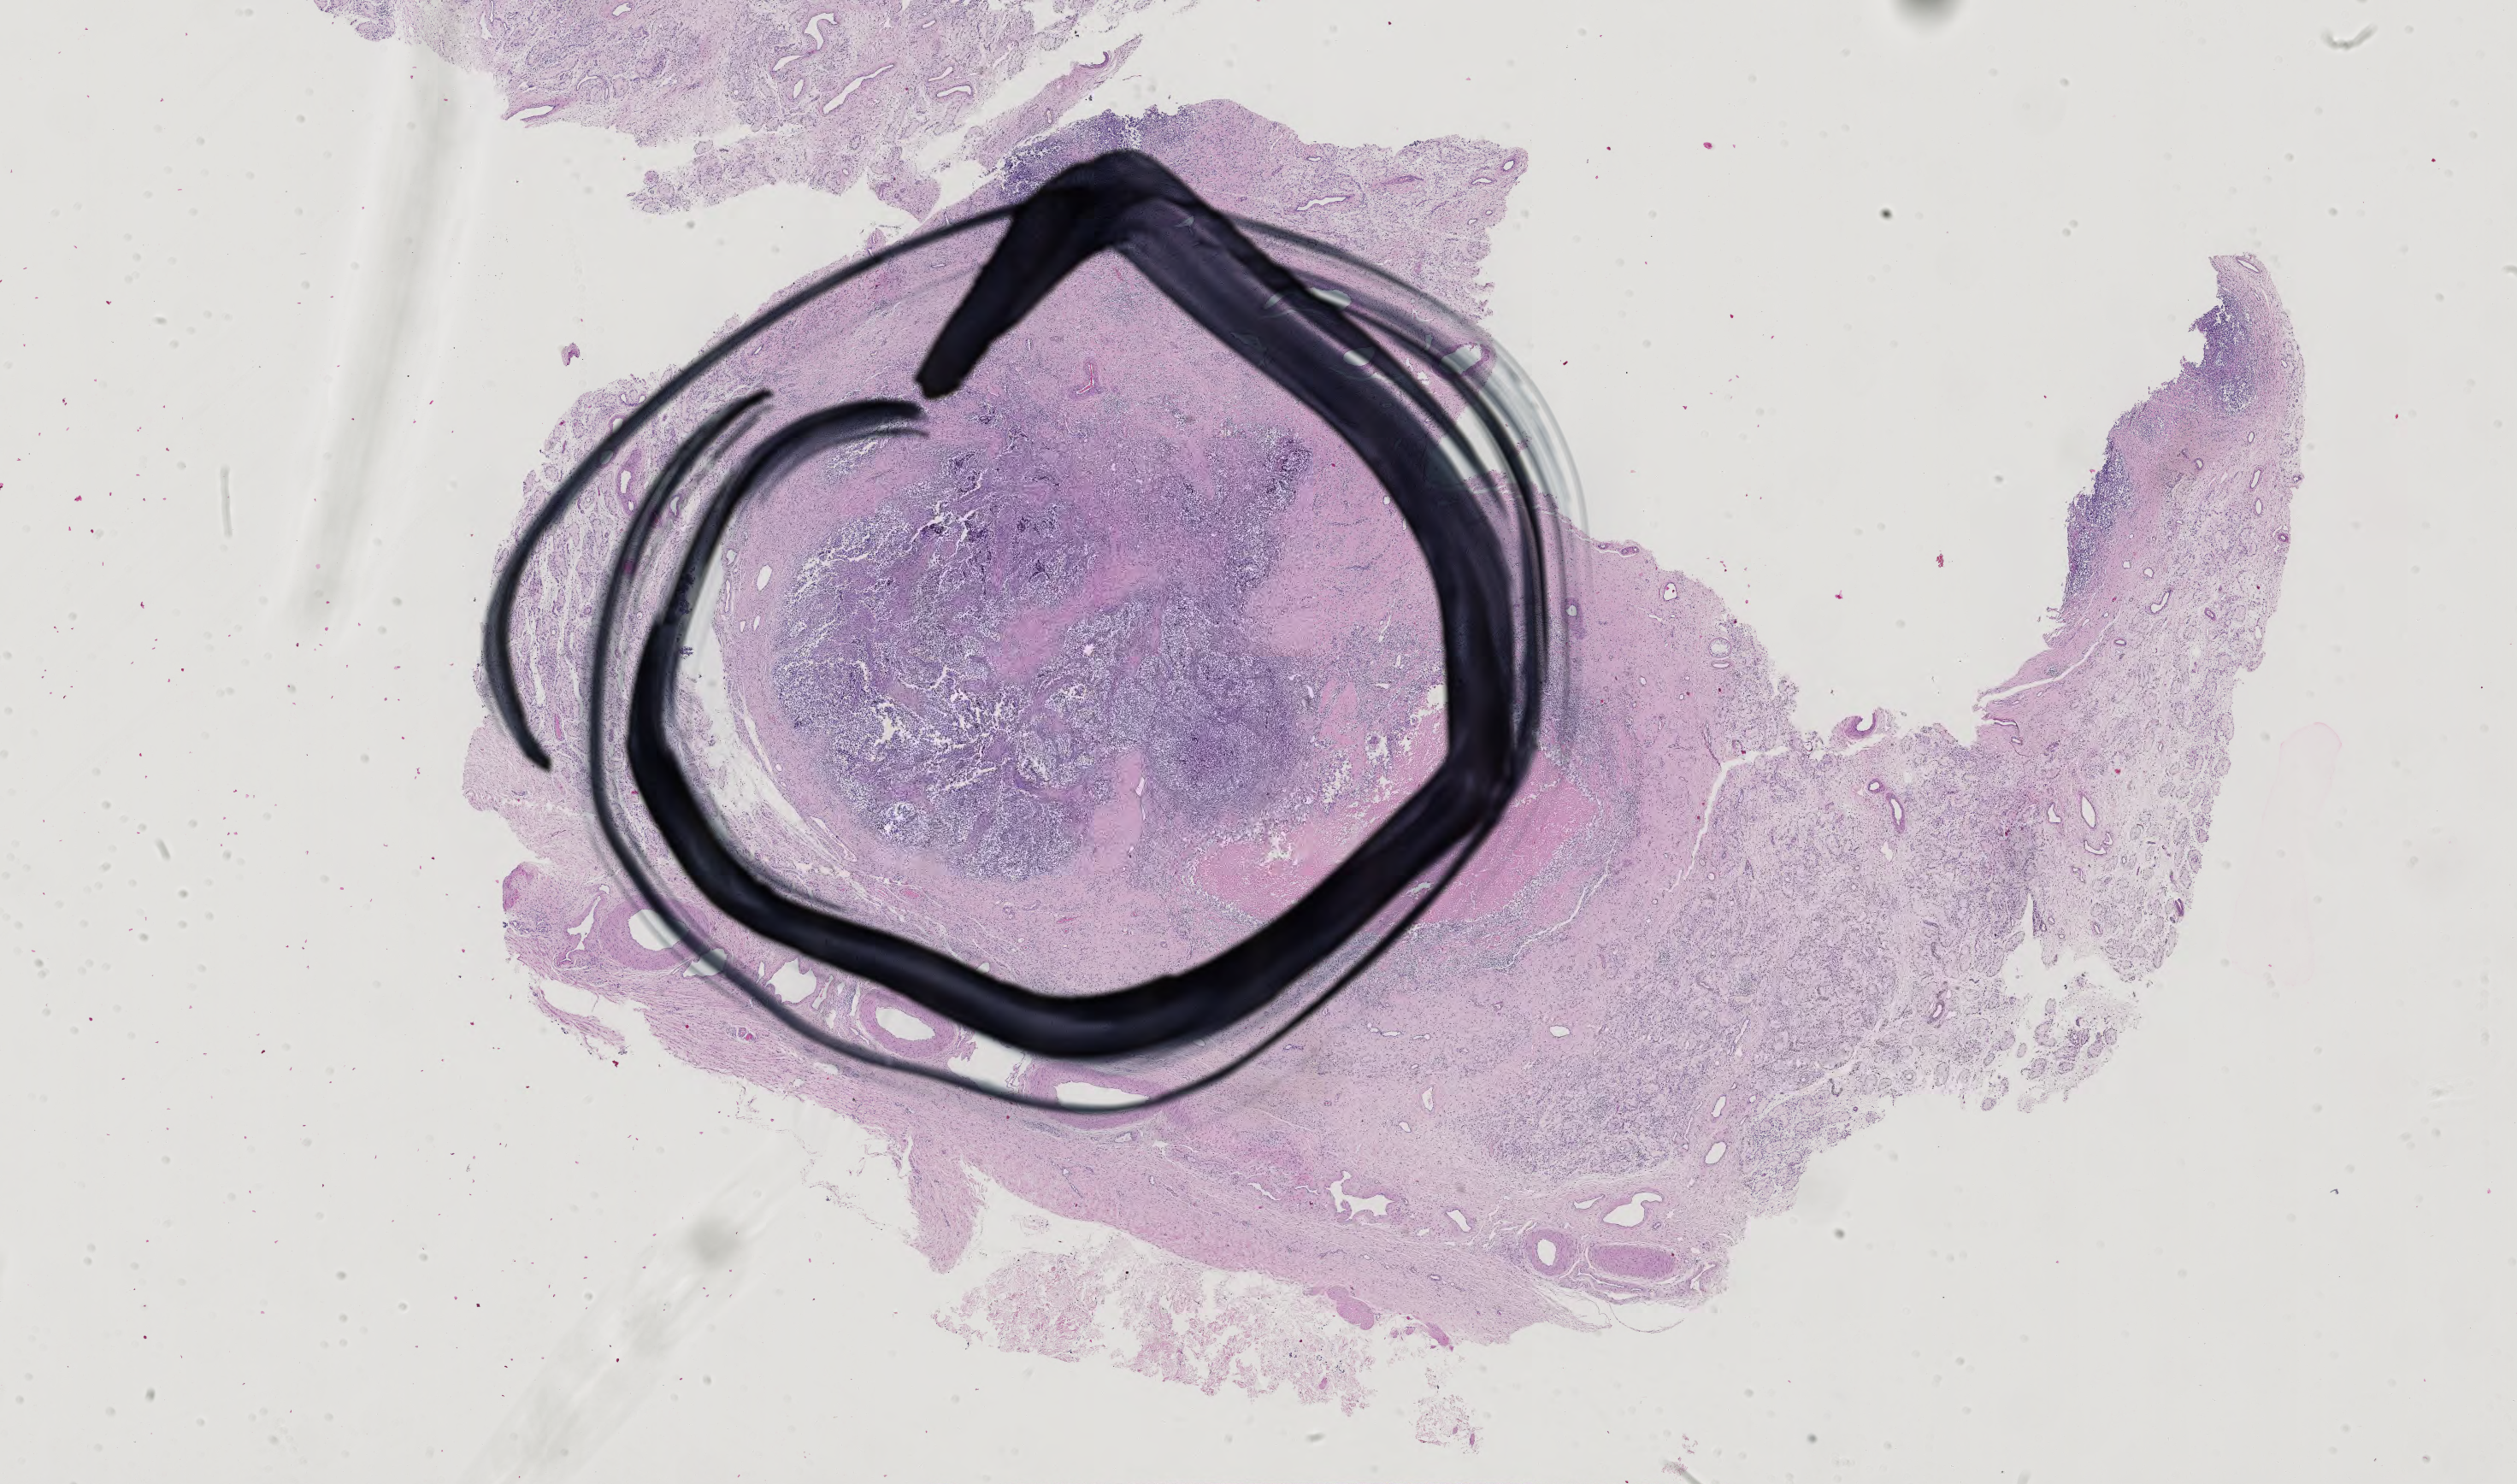
Whole-slide histology image, H&E — whole scanned area (about 21.5 x 12.6 mm, from a 40x scan) shown as a low-resolution overview; FFPE section; sample: primary tumour, testis. Male patient; age at initial diagnosis 38 years.
- laterality: left
- AJCC pathologic stage: IIB
- pathologic diagnosis: Seminoma, NOS